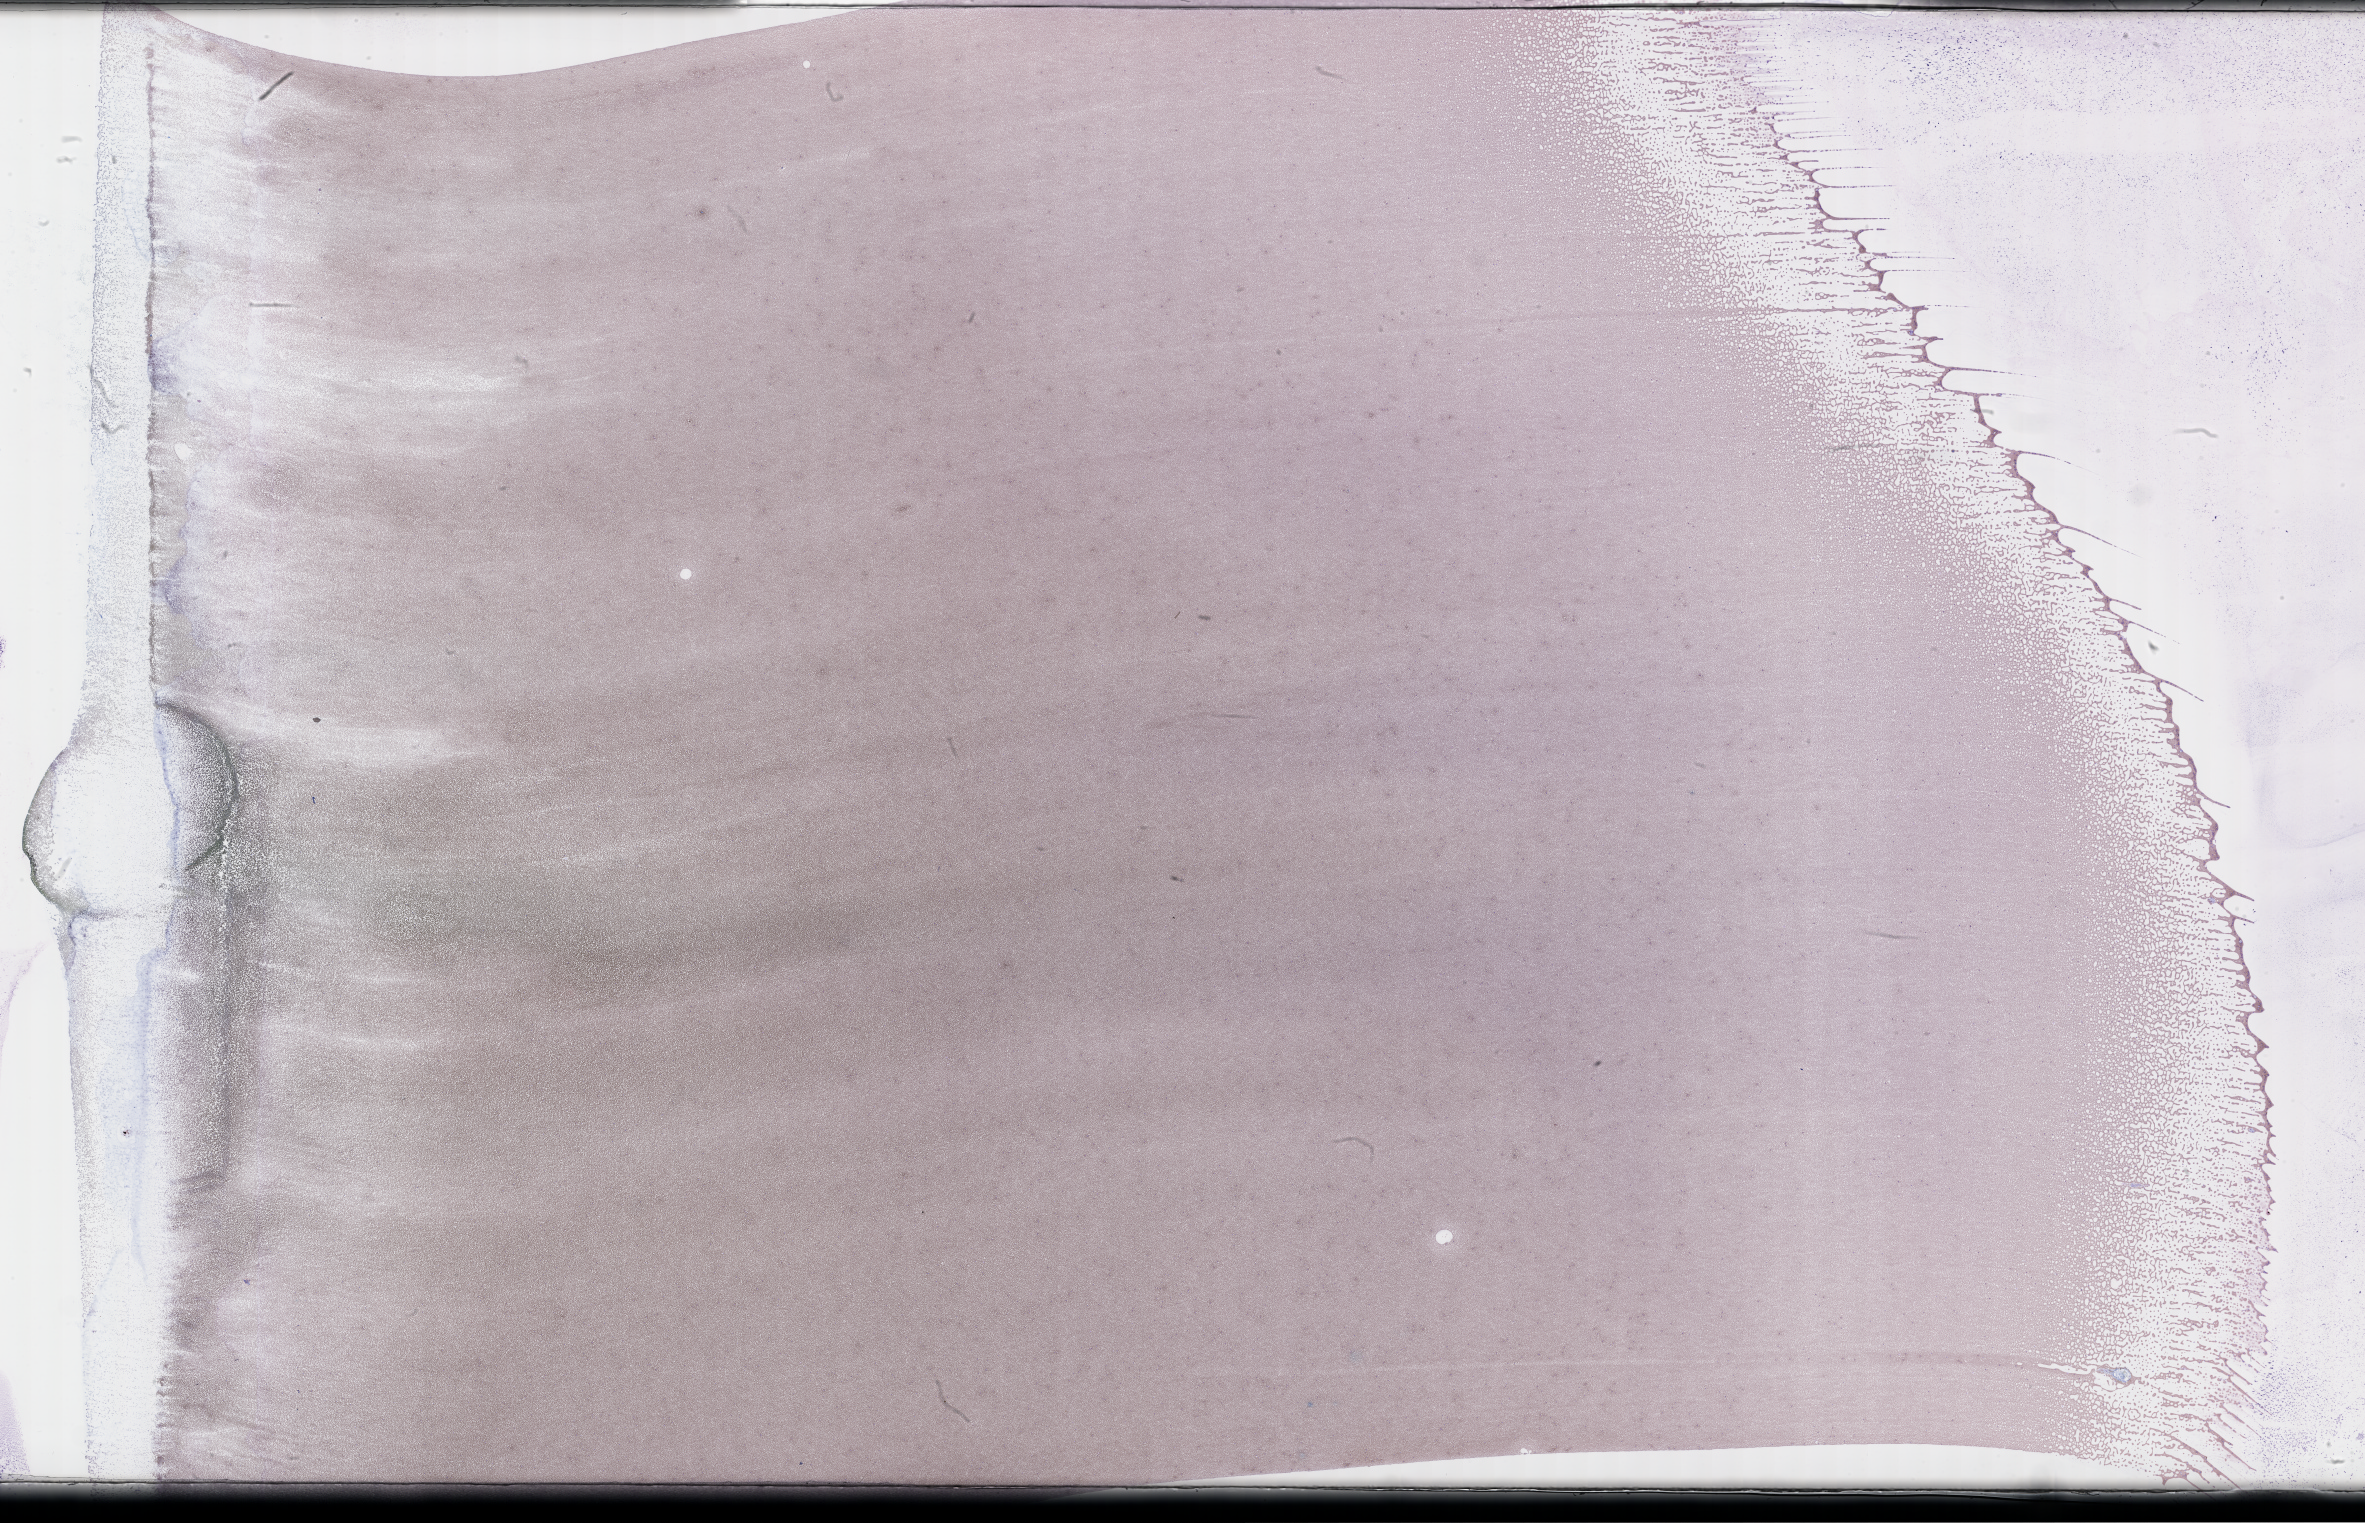
Whole-slide image of a whole blood smear, Wright–Giemsa stain — low-resolution overview of the scanned area, about 38.2 x 24.6 mm, EDTA-anticoagulated smear, collected on treatment. Male patient.
From a patient with: Plasma Cell Myeloma.